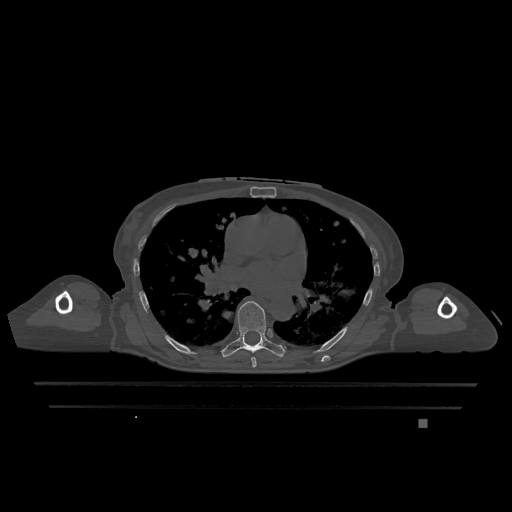
CT including the spine, one axial slice. Slice 748 of 1317 in the series (ordered by position). Bone window (W 1800 / L 400 HU). 0.5 mm slice thickness. 512 × 512 image matrix. Female patient, age 74 years. Case-level facts recorded for this patient, not image findings: primary cancer: lung.
Structures marked on this image (semi-automatic segmentation, software-assisted and operator-edited):
- T6 vertebra: bounding box [x1, y1, x2, y2] px = [251, 357, 257, 368]
- T7 vertebra: [221, 301, 286, 358]